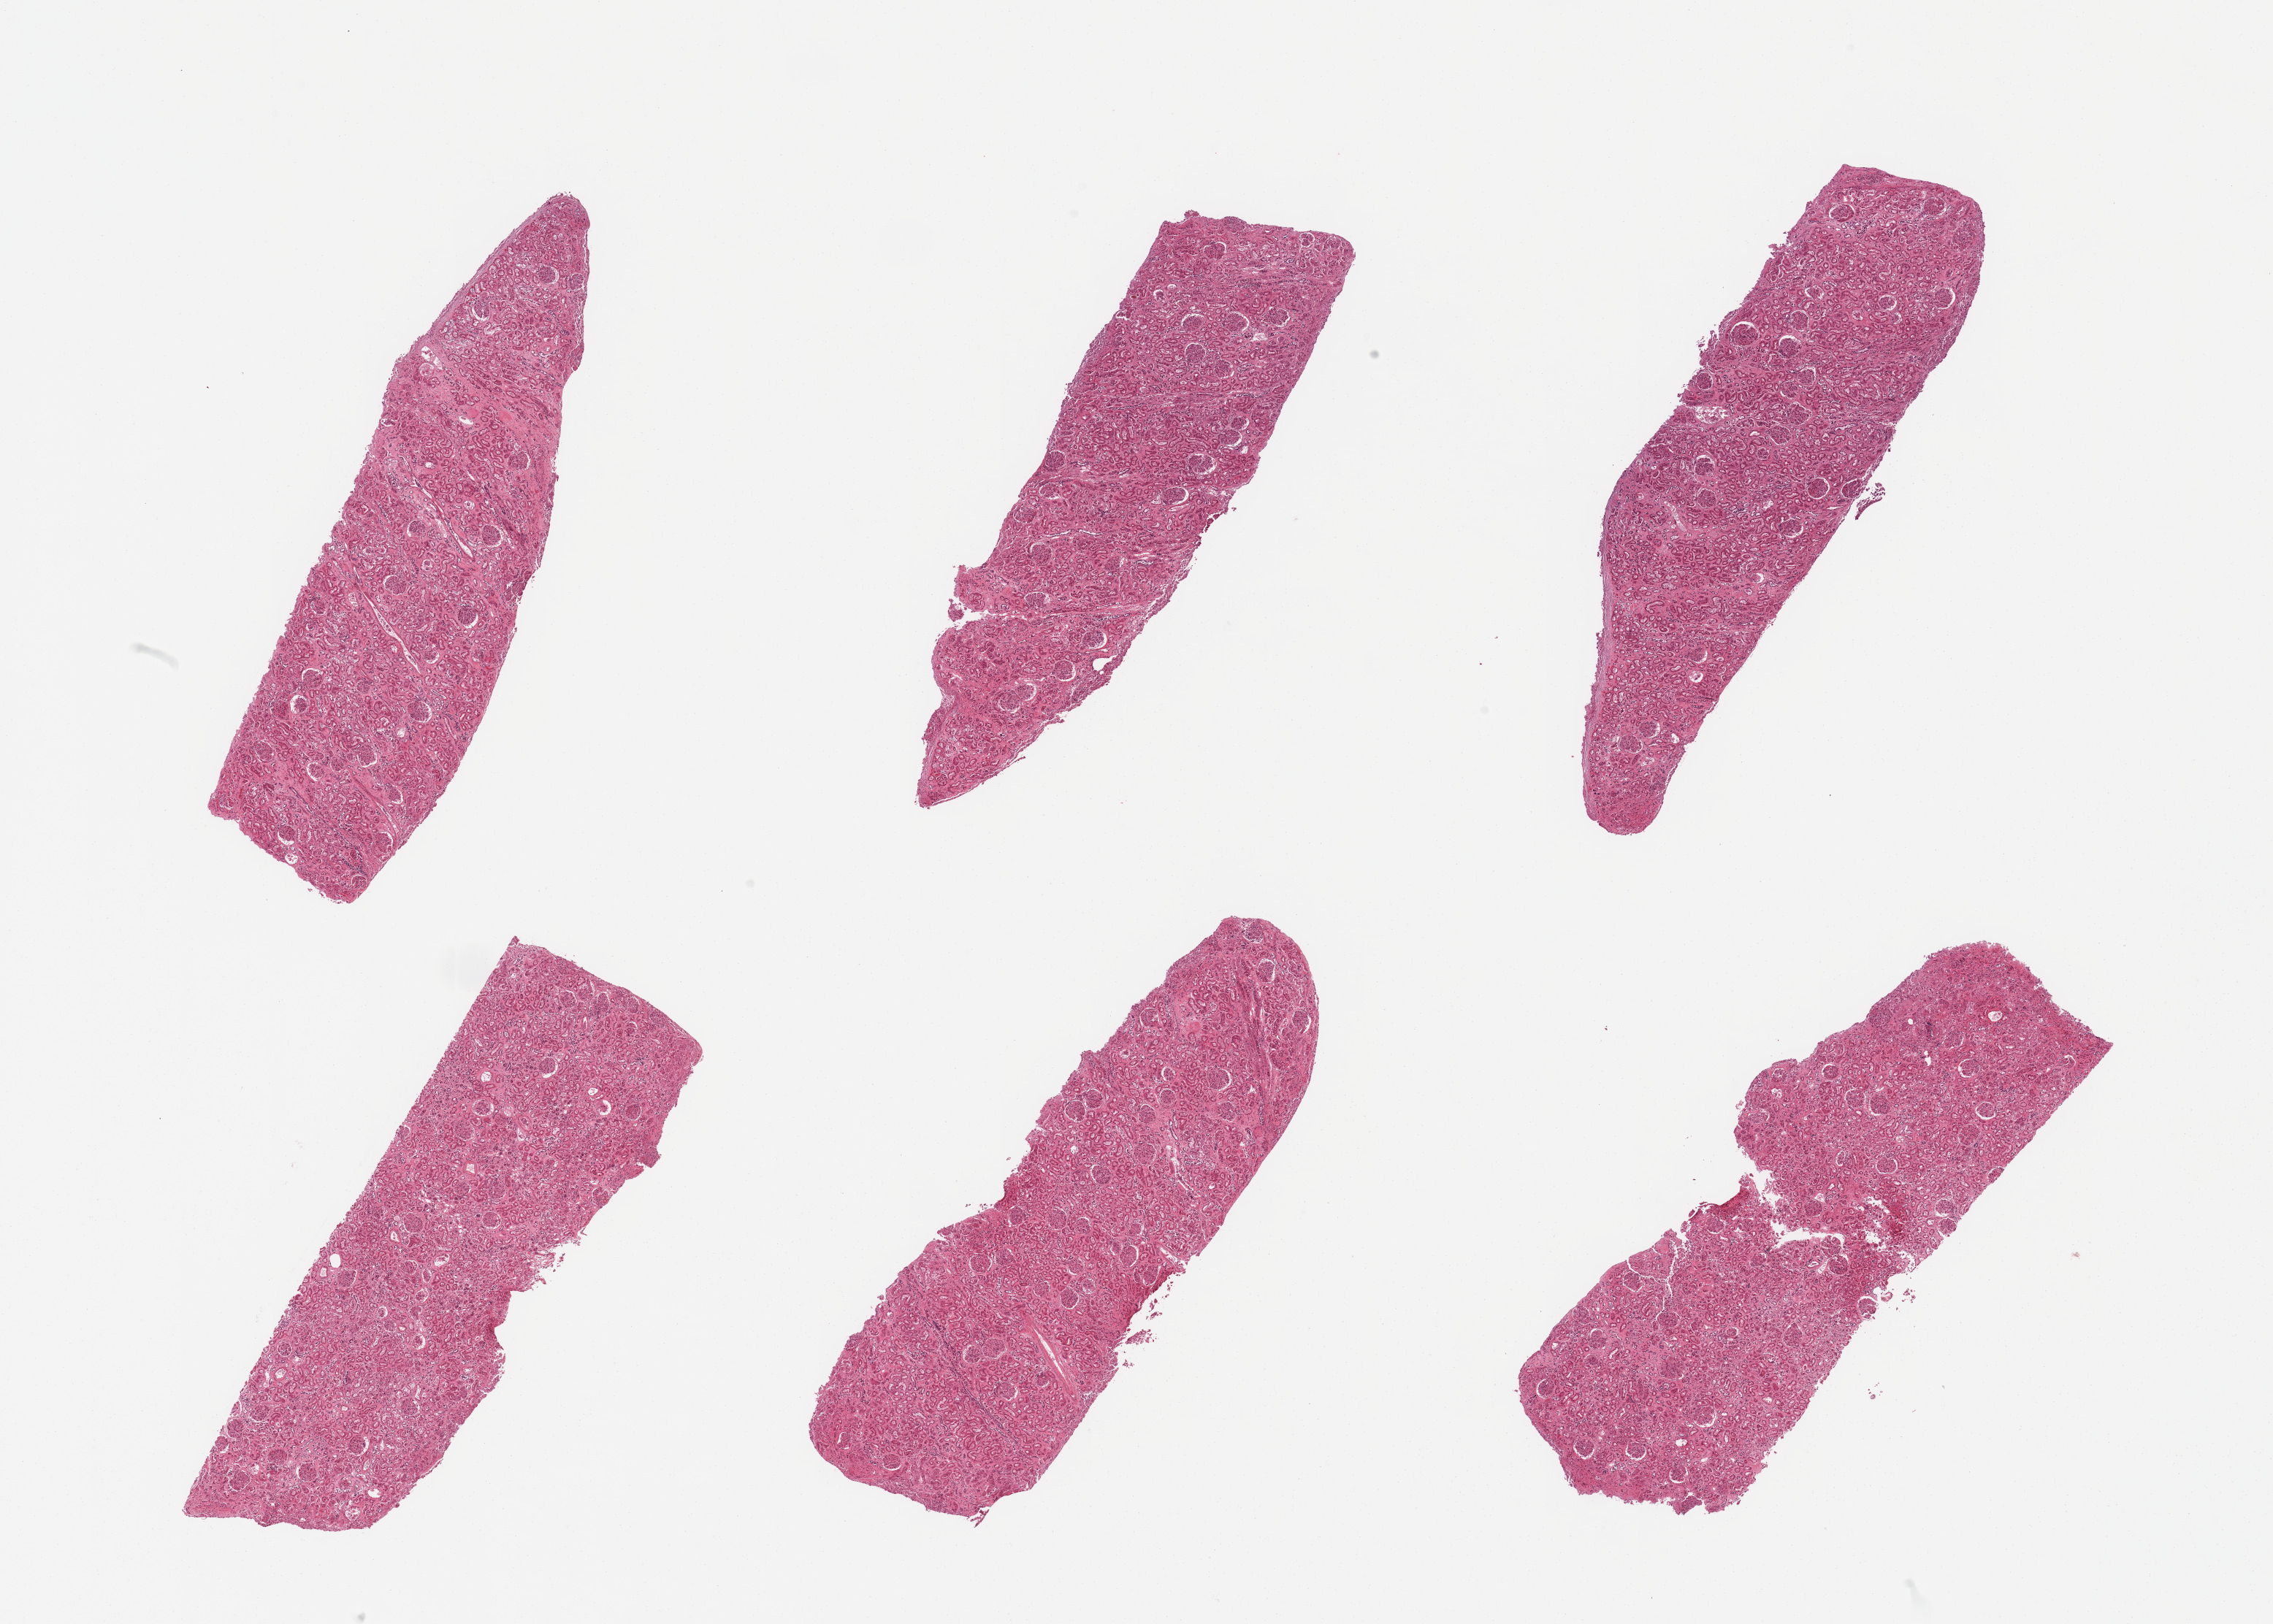
Digitized hematoxylin and eosin (H&E)-stained section, whole scanned area (about 24.6 x 17.6 mm) shown as a low-resolution overview, PAXgene-fixed paraffin-embedded (PFPE) section, section of renal cortex (target tissue), tissue donor sample. Donor sex: male.
Review note (as recorded): 6 pieces; glomeruli in all sections, few sclerotic, arterionephrosclerosis.